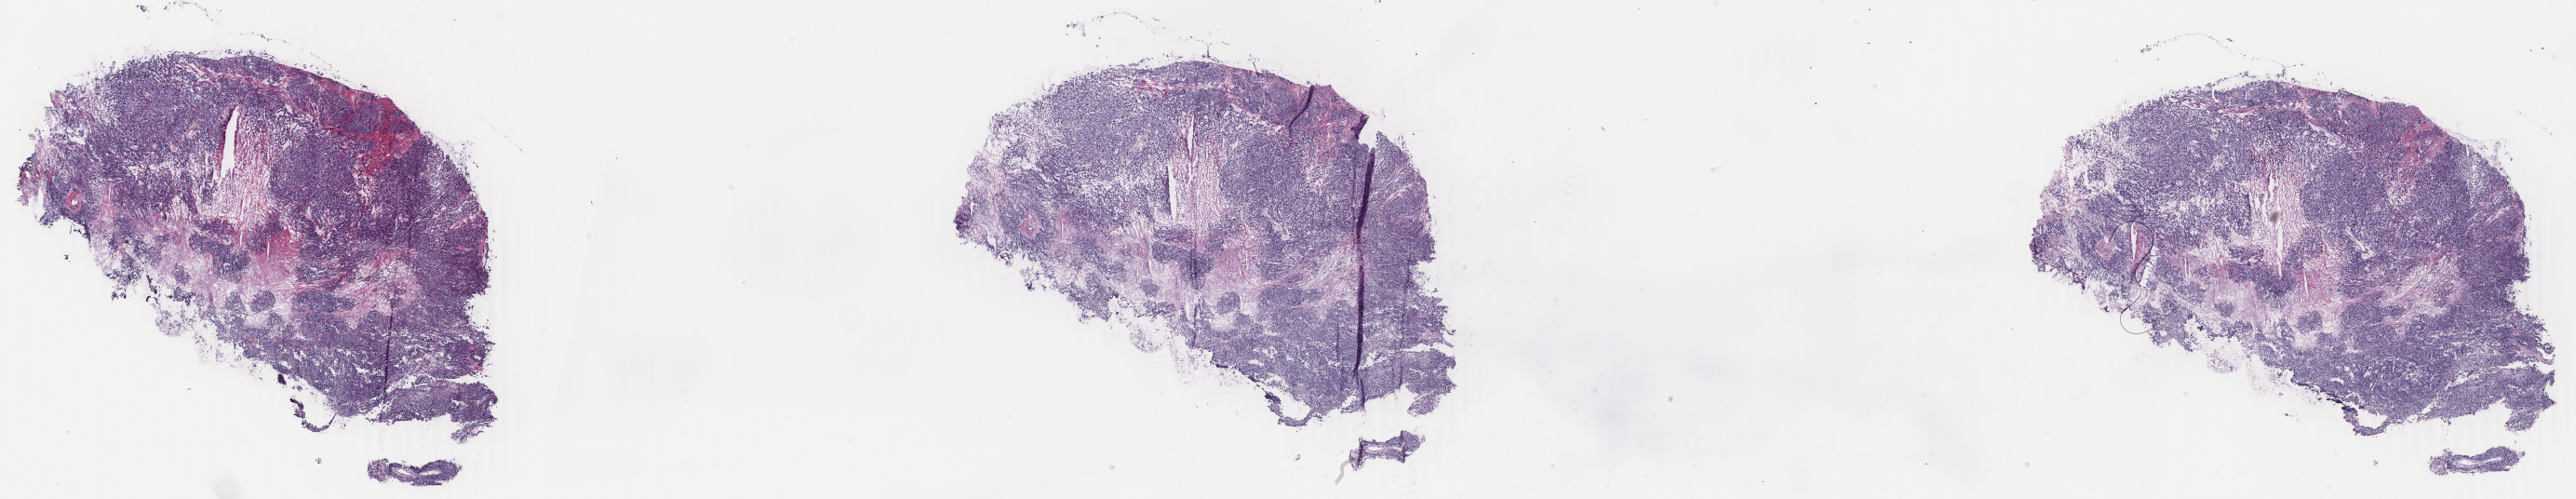
Digitized H&E-stained tissue section (whole slide) — whole scanned area (about 44.0 x 8.5 mm, acquisition: 40x scan) shown as a low-resolution overview. Frozen section from the top of the tissue portion. Sample: primary tumour, uterus. Female patient; age at initial diagnosis 61 years. Histologic grade: G3 (poorly differentiated). Pathologist review of this section (percent, as recorded): tumour cells 80%, tumour nuclei 90%, normal cells 0%, stromal cells 0%, necrosis 20%. Infiltration values recorded for this section: lymphocyte infiltration 0%, monocyte infiltration 0%, neutrophil infiltration 0%.
* FIGO stage: IIIC2
* diagnosis: Serous cystadenocarcinoma, NOS (endometrium)